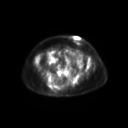
FDG PET of an extremity soft-tissue mass (from a PET/CT study), one axial slice; slice 79 of 267 in the series (ordered by position); 128 × 128 image matrix. Patient: female, 60 years. Case-level facts recorded for this patient, not image findings: histological type: spindle cell suggestive of myxofibrosarcoma; grade: intermediate; site of the primary tumour: right buttock.
Annotated regions visible in this slice (expert contour drawn on MRI and transferred to this co-registered scan by the dataset authors):
- gross tumour volume (mass): bounding box <47,84,62,93> (left, top, right, bottom; pixels)